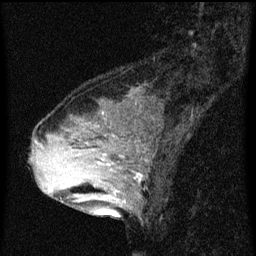
Breast MRI (dynamic contrast-enhanced), one sagittal slice; position 23 of 60 along the scan axis; dynamic contrast-enhanced series, image 2 of 3 at this slice position (ordered by acquisition); 1.5 T; TE 4.2 ms, TR 8 ms; 2 mm slice thickness; 256 × 256 image matrix, field of view 180 × 180 mm. Female patient, age 33 years.
Annotated regions visible in this slice (semi-automatic segmentation, software-assisted and operator-edited):
- analysis volume of interest (the breast-tissue region the enhancement analysis was run in; not a lesion): bounding box (x1, y1, x2, y2) in pixels: (61, 126, 152, 213)
- tumour enhancement mask (voxels above the 70 % enhancement threshold inside the analysis volume of interest): (97, 162, 142, 195)